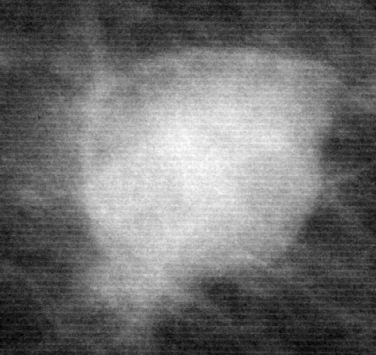
Crop from a digitized film mammogram around one marked abnormality, right breast, CC view.
- Marked abnormality: mass, shape oval, margins microlobulated; BI-RADS assessment category 4; pathology (as recorded): malignant.